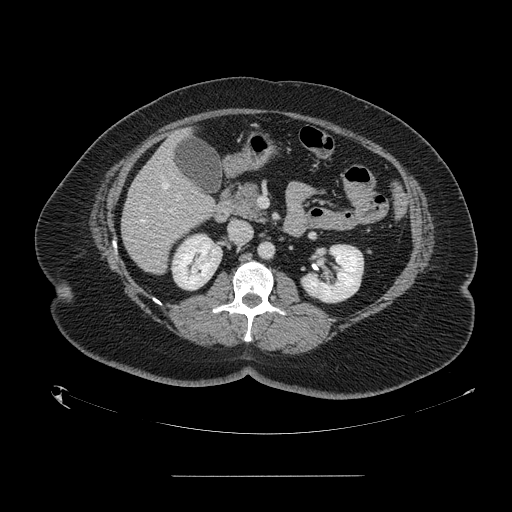
Contrast-enhanced abdominal CT, one axial slice; position 65 of 164 along the scan axis; intravenous contrast given; soft-tissue window (W 400 / L 40 HU); 2.5 mm slice thickness; 512 × 512 image matrix. Female patient, age 52 years. From the clinical record (not read from this slice): diagnosis: colorectal cancer liver metastases, imaged before liver resection; multiple liver metastases: yes; largest metastasis: 3.5 cm; disease in both lobes: no.
Outlined on this slice (outlined manually by an expert reader):
- hepatic veins: box from (x=141, y=183) to (x=174, y=223) px
- liver: (x=122, y=132)–(x=216, y=273)
- portal vein (with intrahepatic branches): (x=176, y=195)–(x=179, y=197)